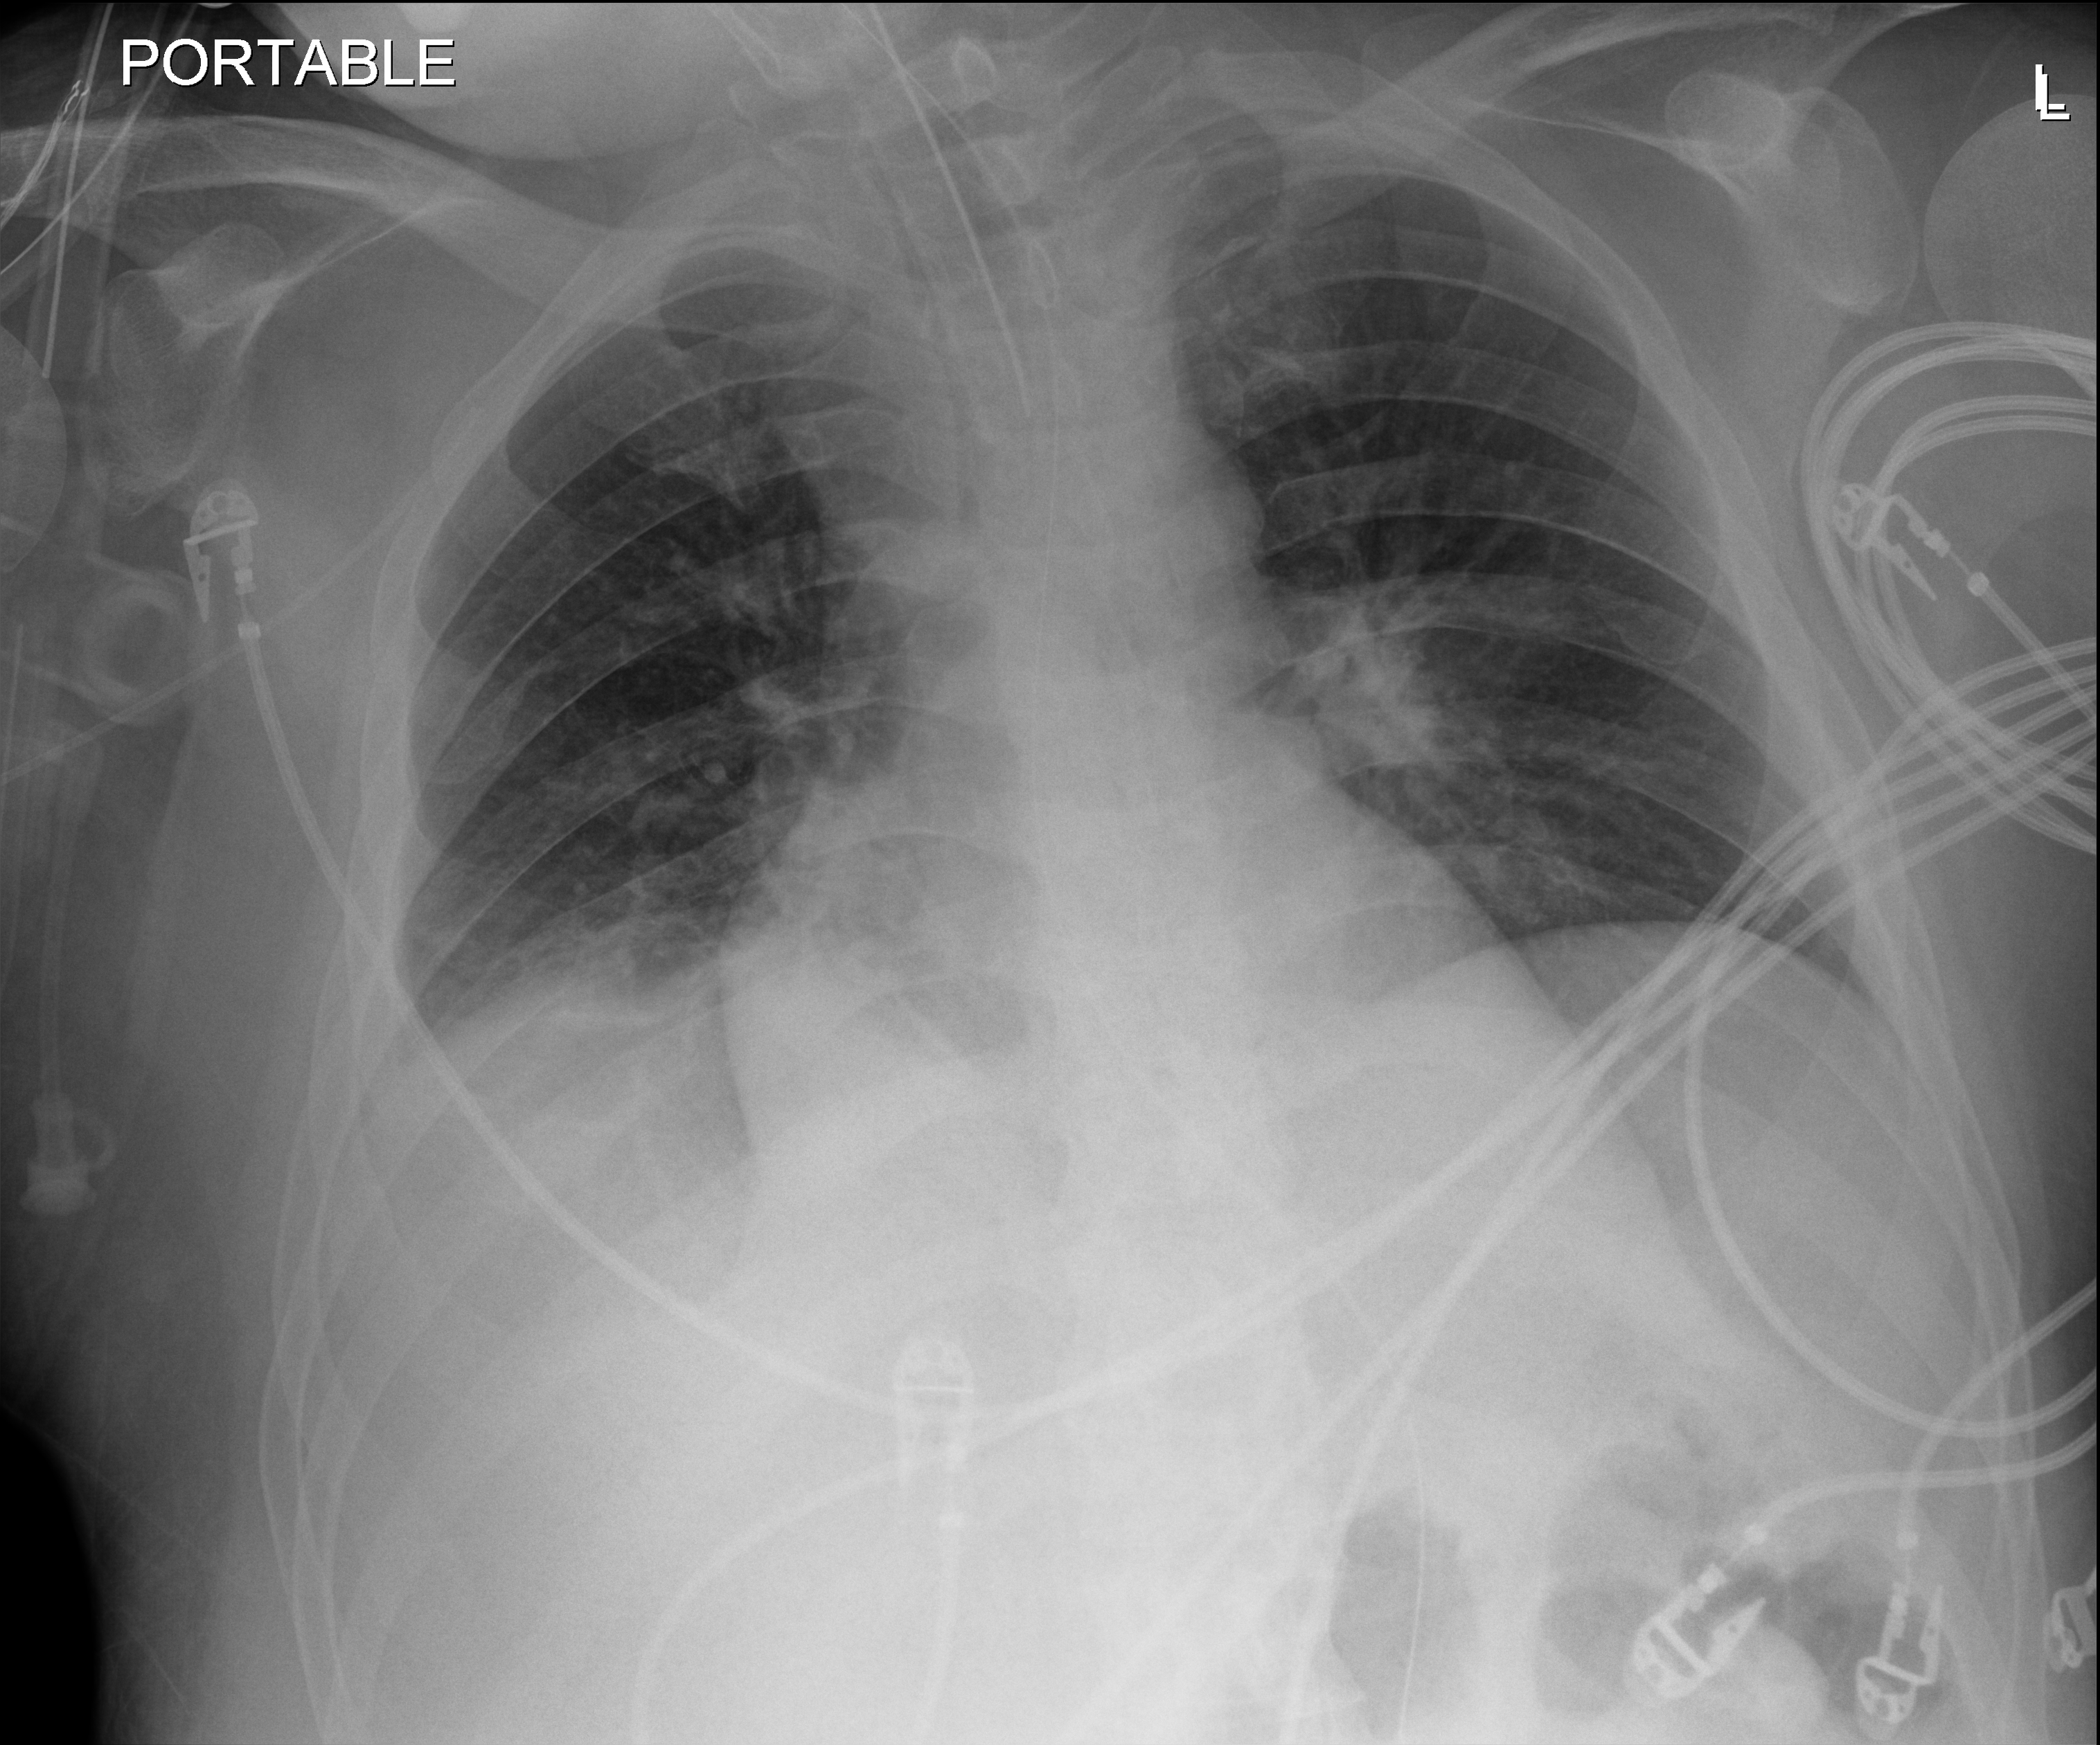
Chest X-ray (portable); anteroposterior (AP) projection. Patient hospitalised with COVID-19; male, aged 18–59 years.
From the hospital-stay record, not from the radiograph (when in the stay this image was taken is not recorded):
- admitted to intensive care during this hospital stay: yes